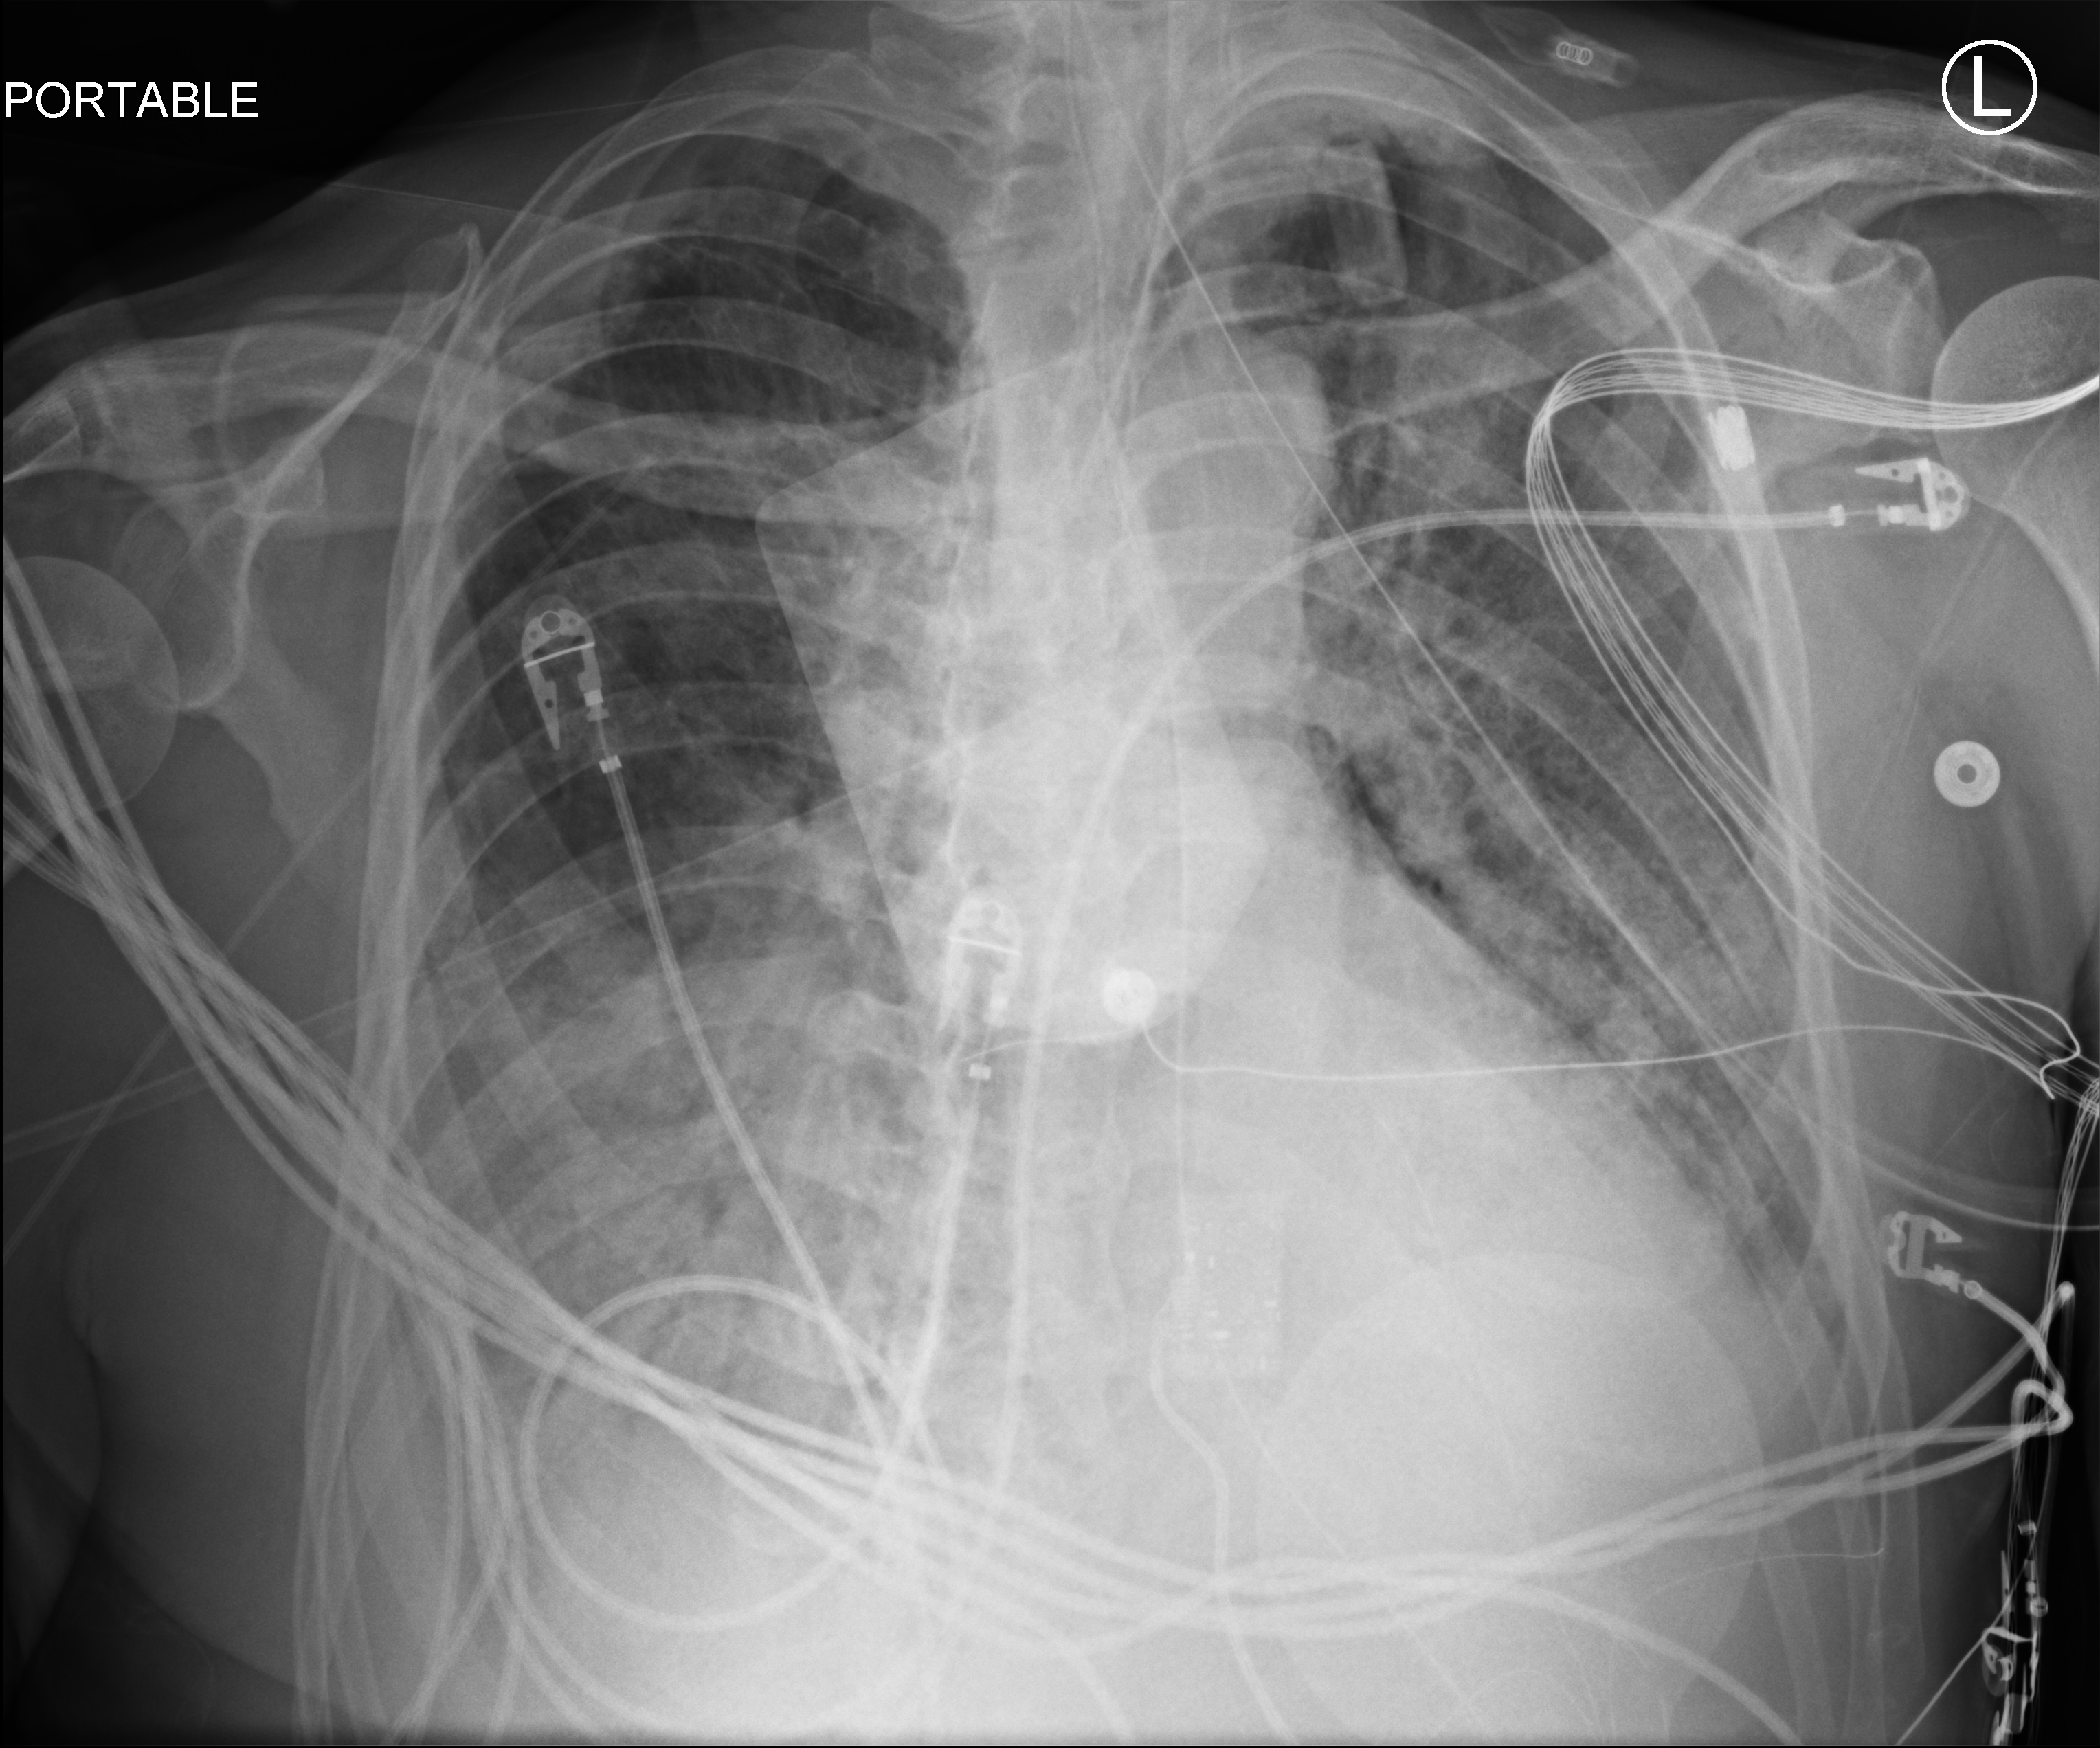
Chest X-ray (portable), anteroposterior (AP) projection. Patient hospitalised with COVID-19; male, aged 60–74 years.
Admission-level facts for this patient (not findings on this image; timing relative to this image not recorded): hypertension (admission record): no; admitted to intensive care during this hospital stay: yes; chronic kidney disease (admission record): no.